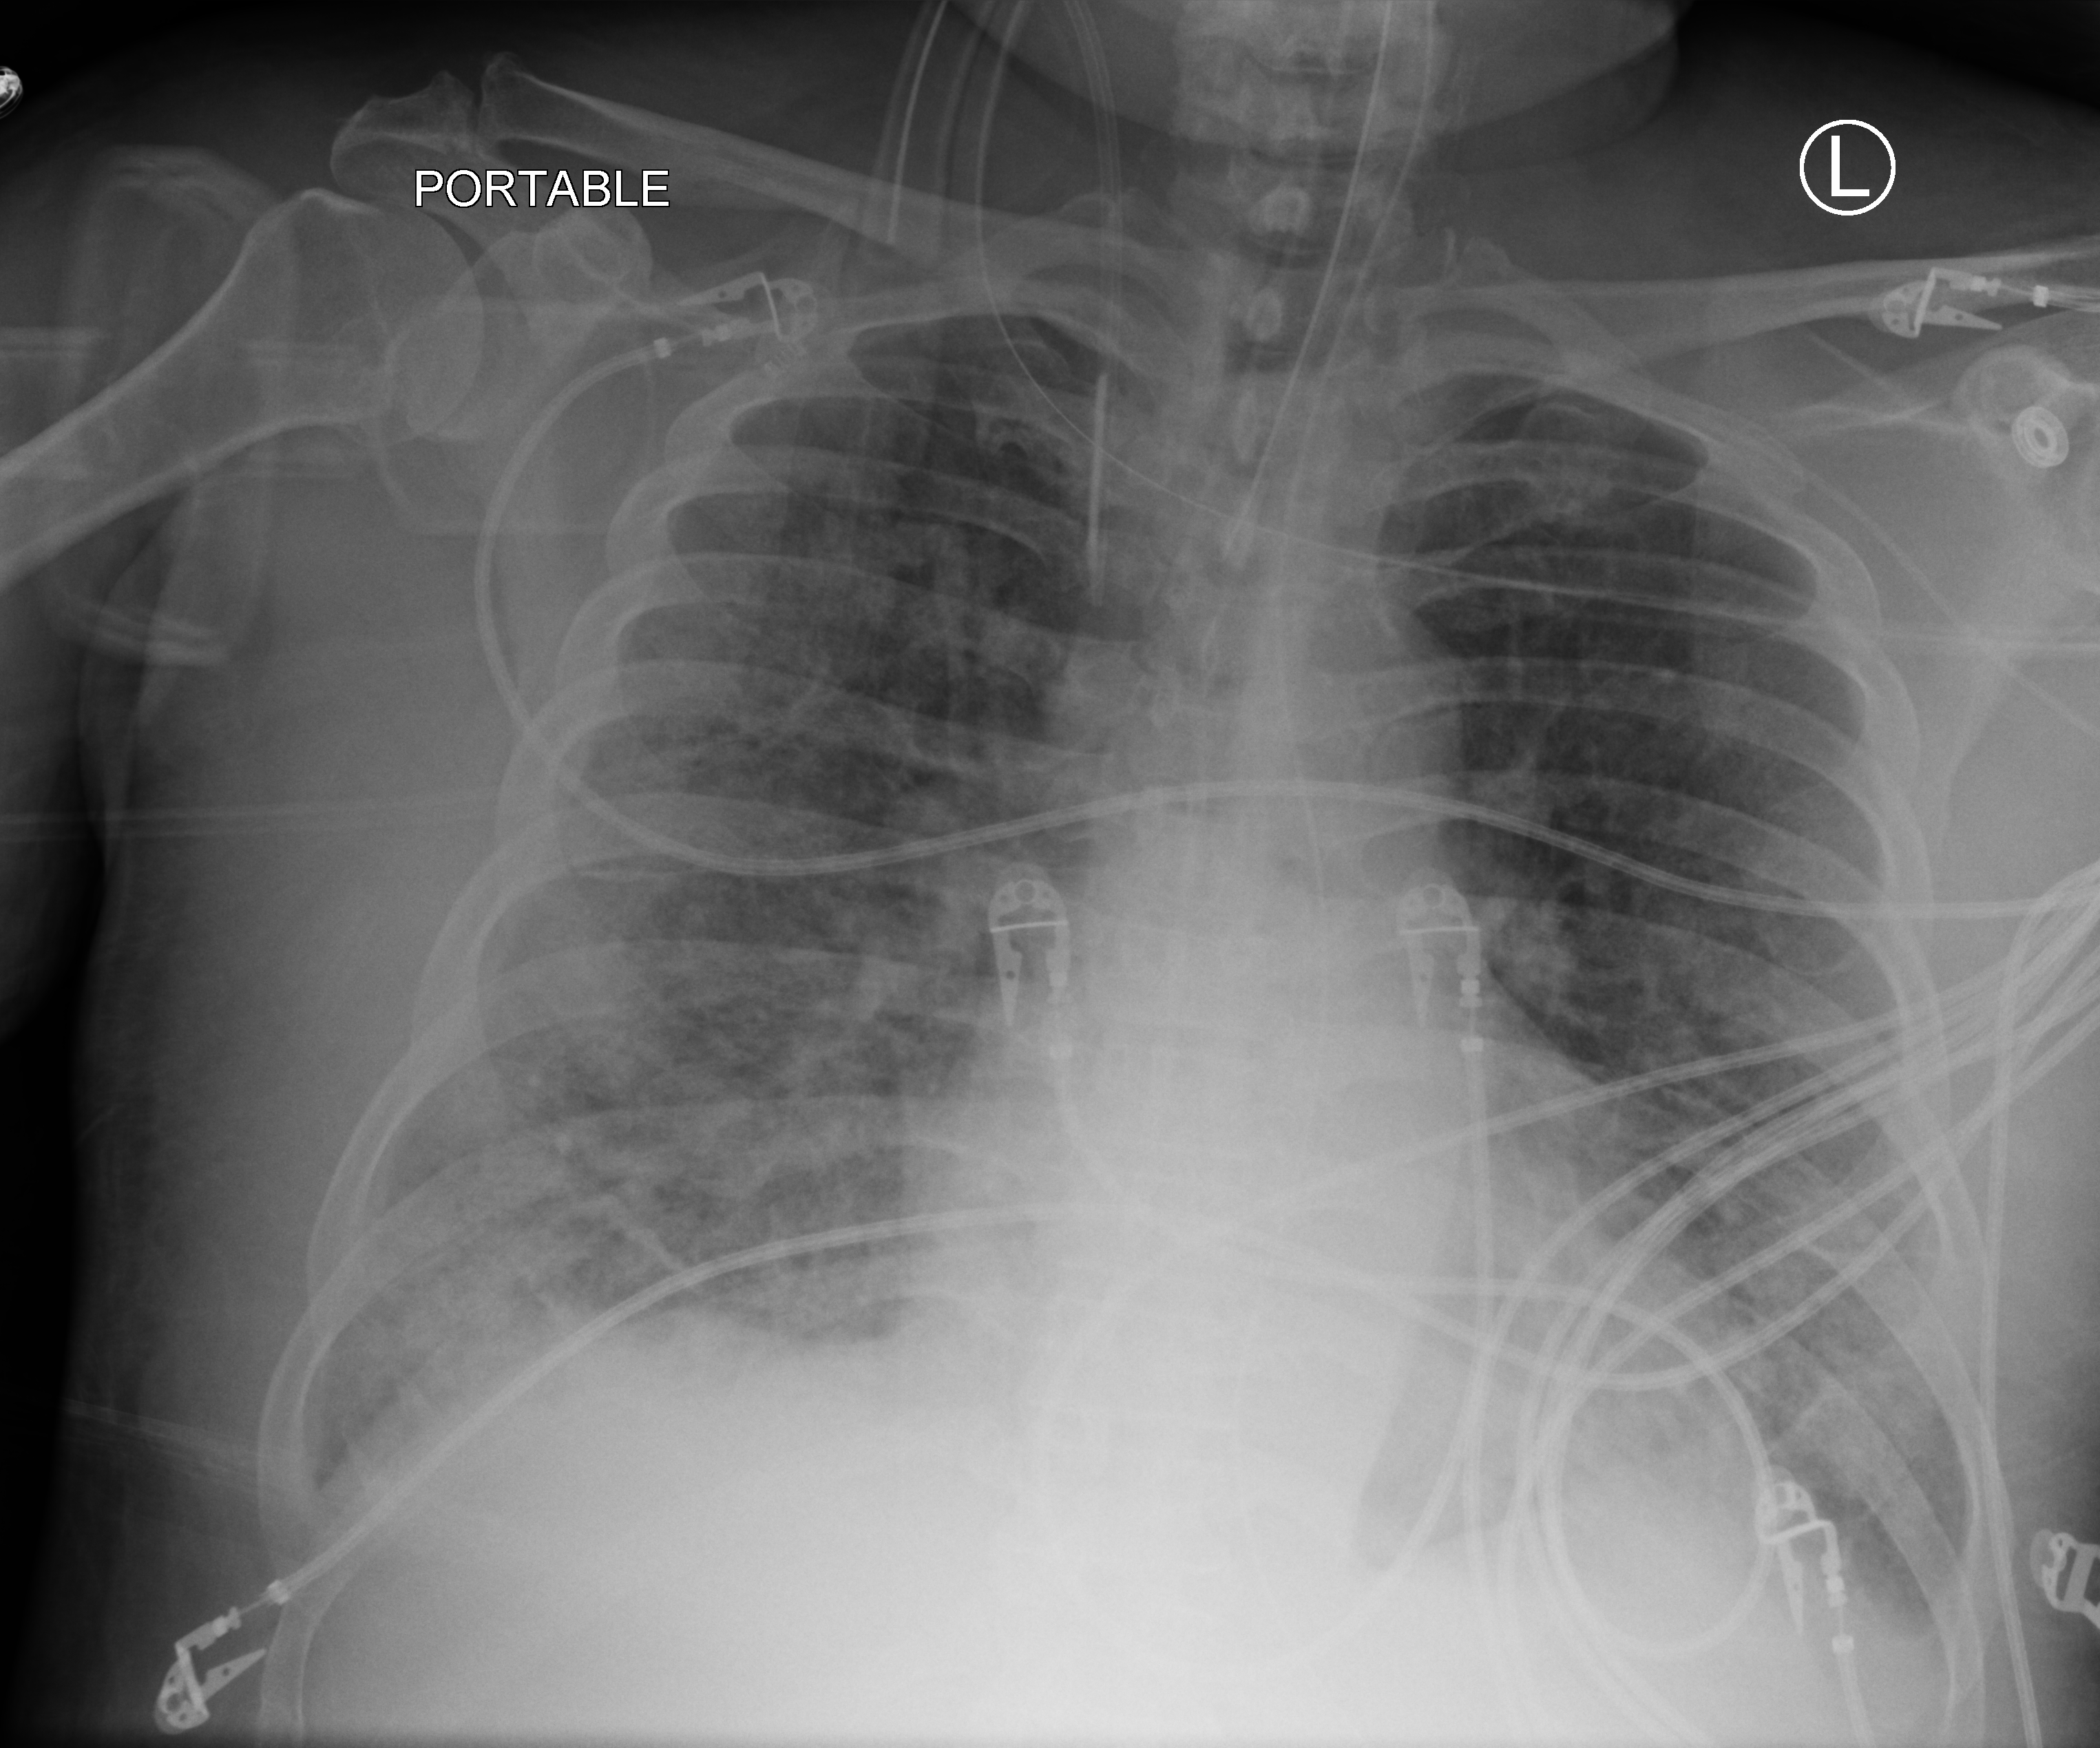
Bedside chest radiograph (computed radiography); anteroposterior (AP) projection. Patient hospitalised with COVID-19; male, aged 60–74 years.
Admission-level facts for this patient (not findings on this image; timing relative to this image not recorded): length of hospital stay: 28 days; mechanically ventilated during this hospital stay: yes; admitted to intensive care during this hospital stay: yes.